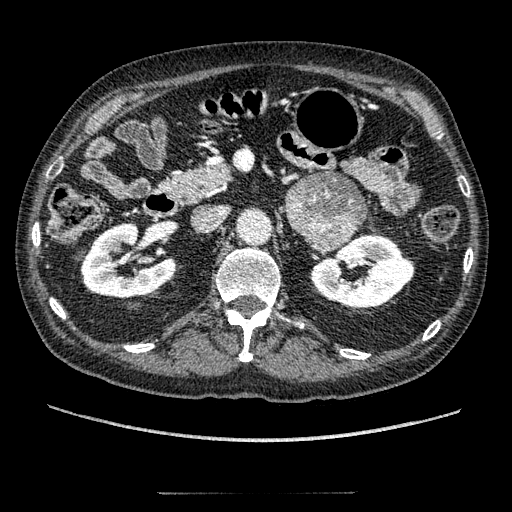
Contrast-enhanced abdominal CT, one axial slice. Position 108 of 274 along the scan axis. Reconstruction kernel STANDARD. 120 kVp. Soft-tissue window (W 400 / L 40 HU). 1.25 mm slice thickness. 512 × 512 image matrix, field of view 381 × 381 mm. Male patient, age 69 years. Case-level facts recorded for this patient, not image findings: diagnosis: adrenocortical carcinoma; tumour side: left adrenal; tumour size at pathology: 6.1 cm; Ki-67 index: 10 %; stage (as recorded): 3.
Outlined on this slice (semi-automatic segmentation, software-assisted and operator-edited):
- mass: box from (x=287, y=173) to (x=366, y=252) px